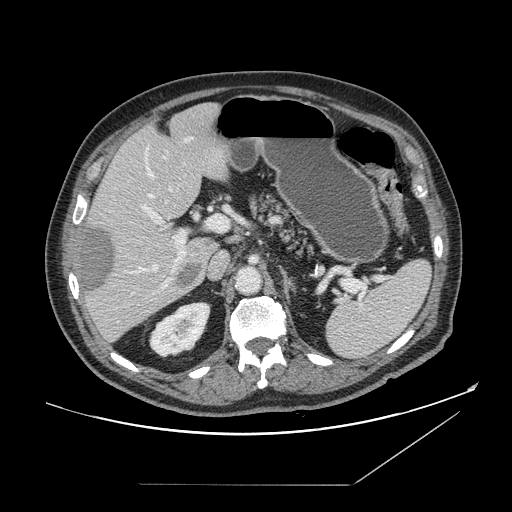
Contrast-enhanced abdominal CT, one axial slice. Position 95 of 166 along the scan axis. 120 kVp. Intravenous contrast given. Soft-tissue window (W 400 / L 40 HU). 2.5 mm slice thickness. 512 × 512 image matrix. Male patient, age 80 years. From the clinical record (not read from this slice): diagnosis: colorectal cancer liver metastases, imaged before liver resection; multiple liver metastases: no; largest metastasis: 2.2 cm; chemotherapy before resection: no.
Annotated regions visible in this slice (expert manual segmentation):
- hepatic veins: bounding box (x1, y1, x2, y2) in pixels: (136, 150, 172, 273)
- liver: (76, 103, 231, 342)
- planned liver remnant (the part of the liver to remain after resection): (94, 103, 231, 254)
- portal vein (with intrahepatic branches): (141, 206, 230, 289)
- liver metastasis: (80, 225, 201, 296)